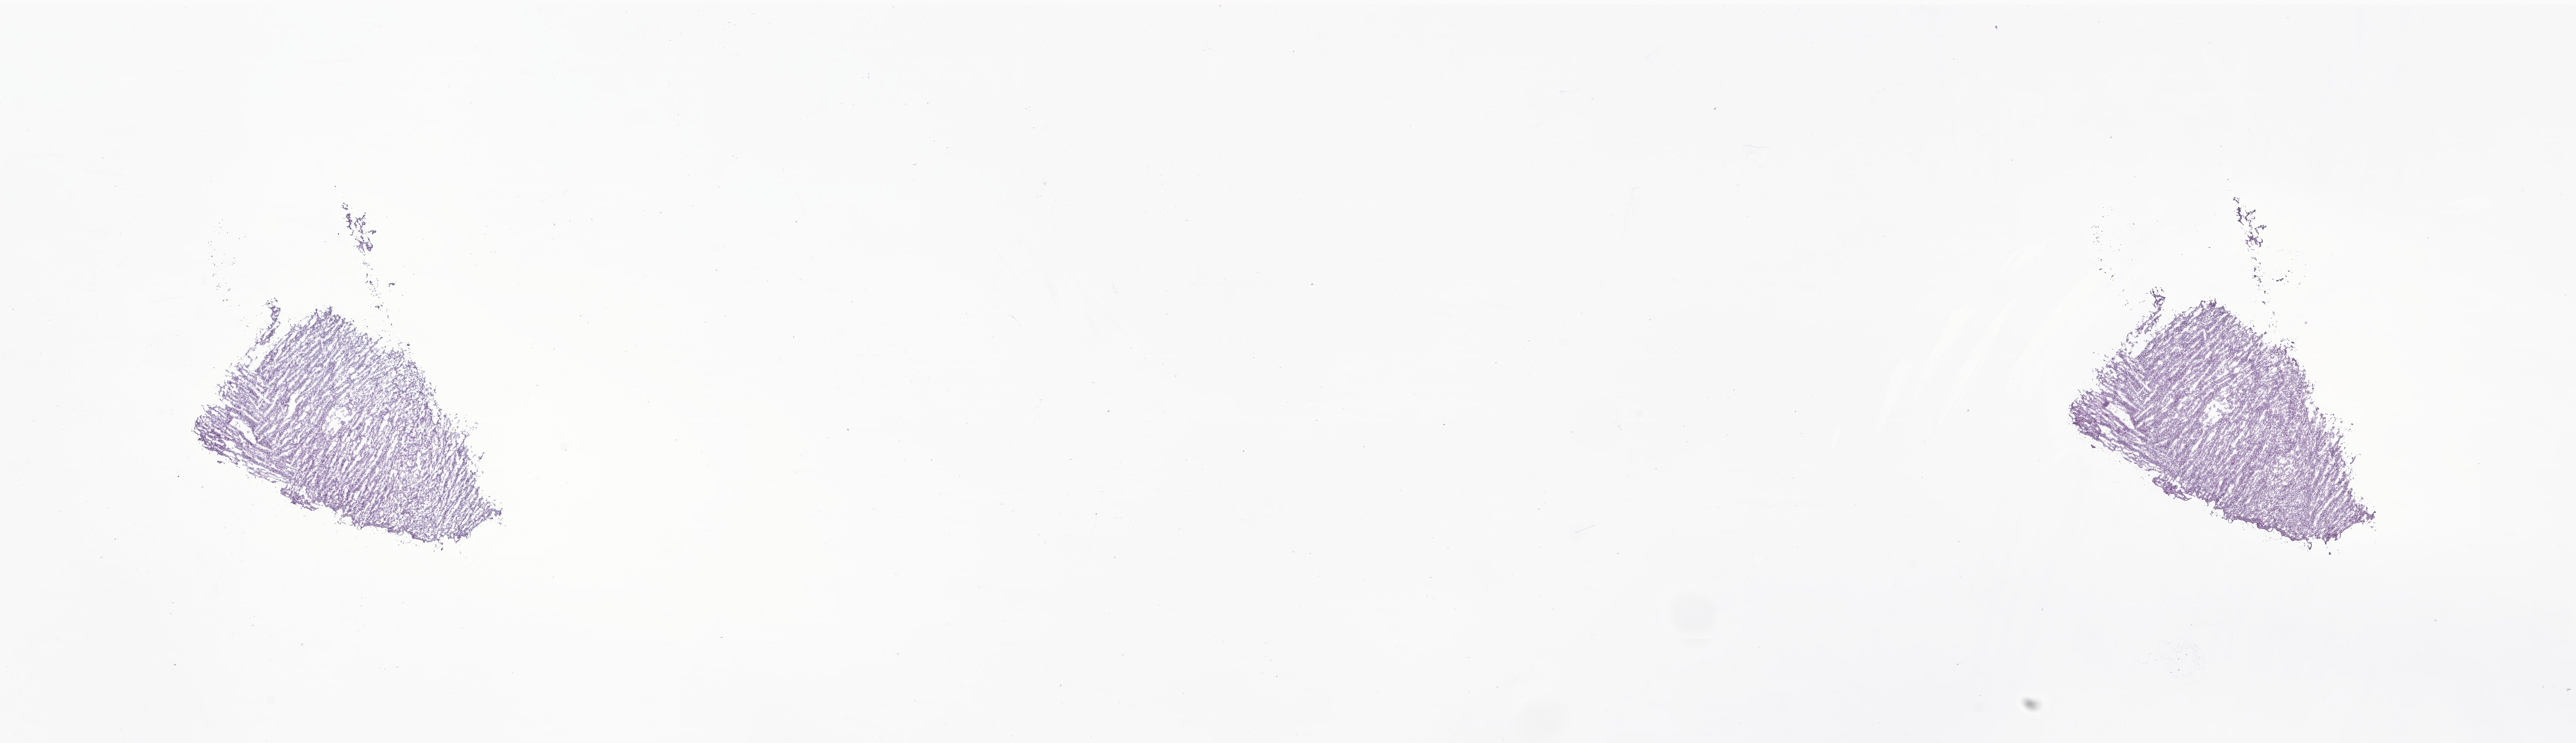
Whole-slide image, haematoxylin and eosin stain of tumor tissue from the ovary — shown as a low-resolution overview of the whole scanned area (about 25.3 x 7.3 mm), cryosection (OCT / tissue freezing medium). Patient: female, age 200 months (16 years 8 months).
Recorded diagnosis: Small cell carcinoma, NOS.